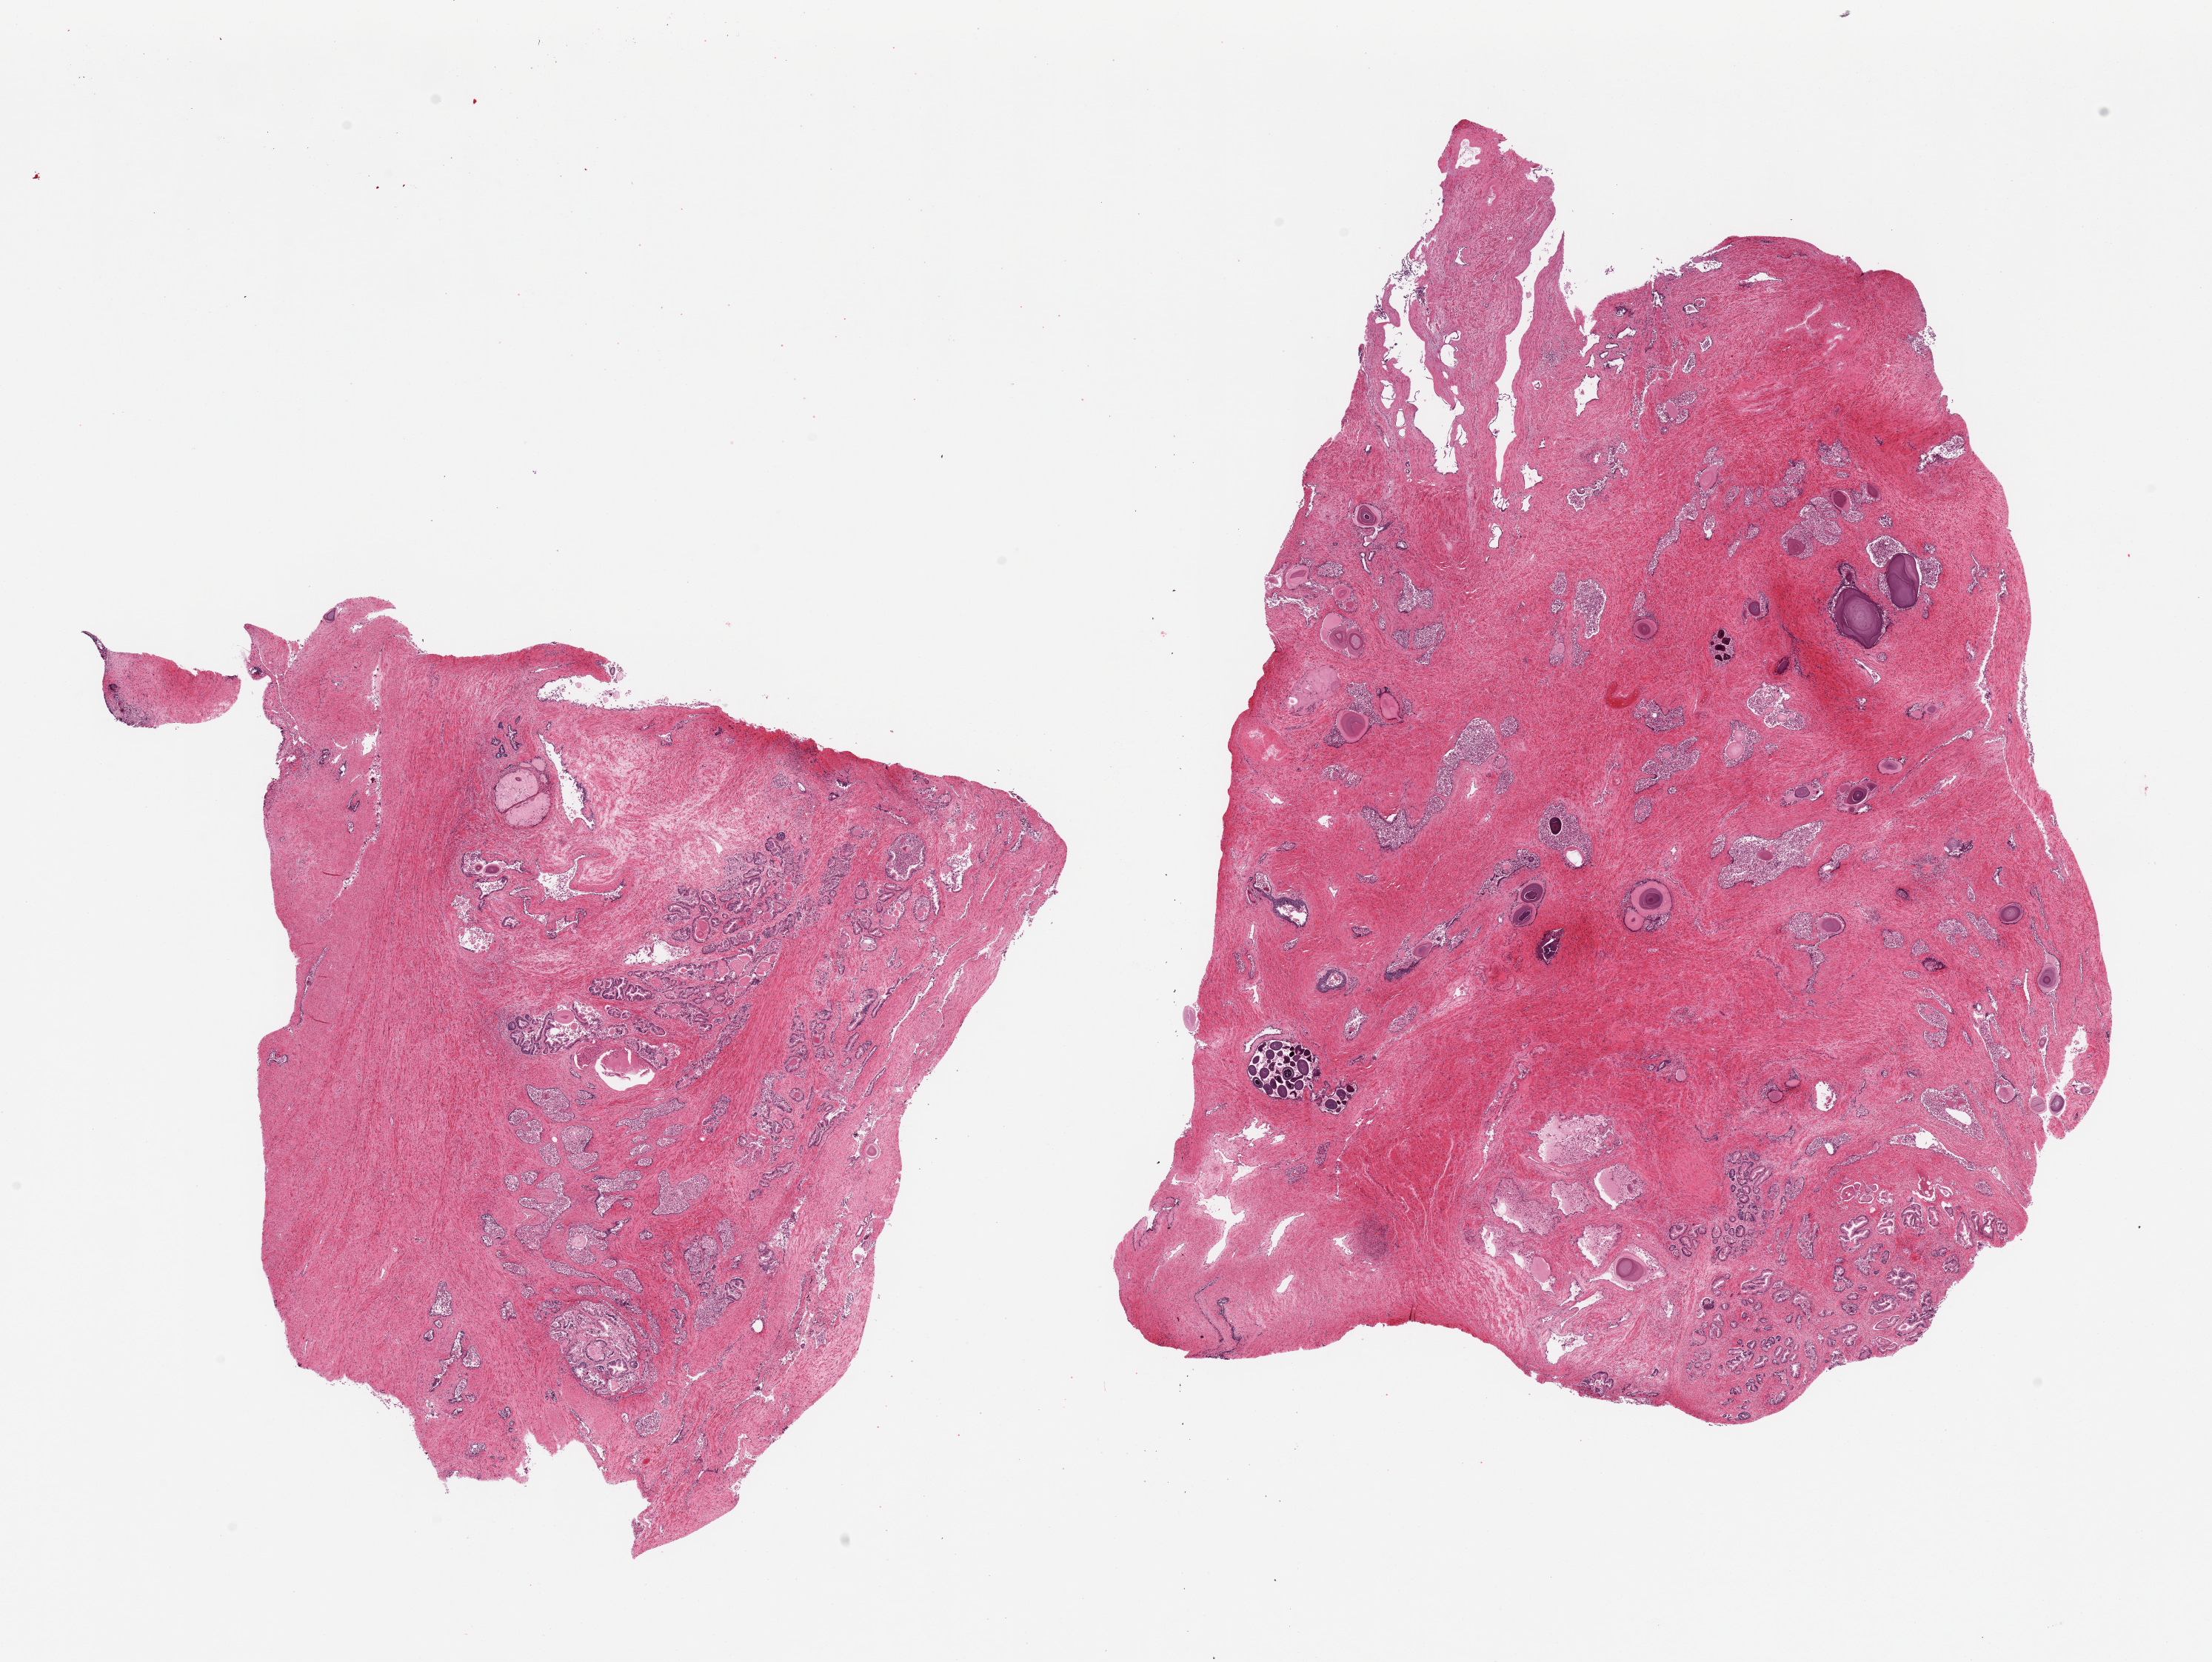
Haematoxylin and eosin whole-slide image — low-resolution overview of the scanned area, about 23.6 x 17.7 mm; PAXgene-fixed, paraffin-embedded tissue; target tissue: prostate; donor tissue sample. Male donor.
• review note (as recorded): 2 pieces; glands vary from moderate to severe autolysis